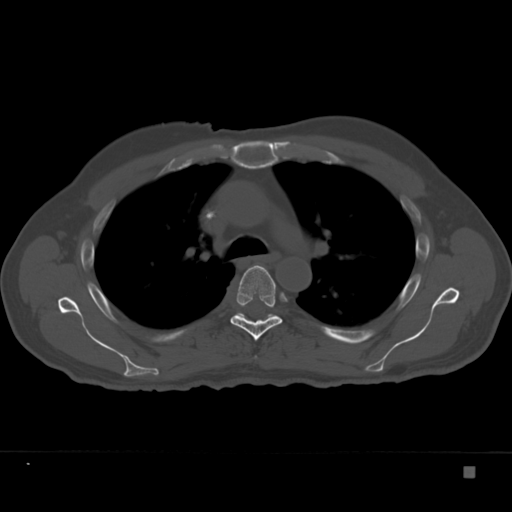
CT including the spine, one axial slice. Slice 256 of 332 in the series (ordered by position). 120 kVp. Bone window (W 1800 / L 400 HU). 1.5 mm slice thickness. 512 × 512 image matrix, field of view 389 × 389 mm. Patient: male, 72 years. Case-level facts recorded for this patient, not image findings: primary cancer: skeletal.
Outlined on this slice (semi-automatically segmented with operator editing):
- T5 vertebra: bounding box (x1, y1, x2, y2) in pixels: (230, 265, 282, 341)
- T6 vertebra: (236, 312, 276, 318)